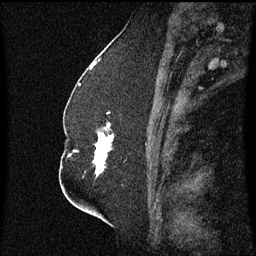
Breast MRI (dynamic contrast-enhanced), one sagittal slice; slice 31 of 60 in the series (ordered by position); dynamic contrast-enhanced series, image 2 of 3 at this slice position (ordered by acquisition); 1.5 T; TE 4.2 ms, TR 8.4 ms; 2.3 mm slice thickness; 256 × 256 image matrix. Patient: female, 52 years. From the clinical record (not read from this slice): setting: breast cancer imaged before/during neoadjuvant chemotherapy; receptor status: HR-positive, HER2-negative.
Annotated regions visible in this slice (semi-automatic segmentation, software-assisted and operator-edited):
- analysis volume of interest (the breast-tissue region the enhancement analysis was run in; not a lesion): bounding box (x1, y1, x2, y2) in pixels: (75, 114, 126, 177)
- tumour enhancement mask (voxels above the 70 % enhancement threshold inside the analysis volume of interest): (93, 124, 113, 175)